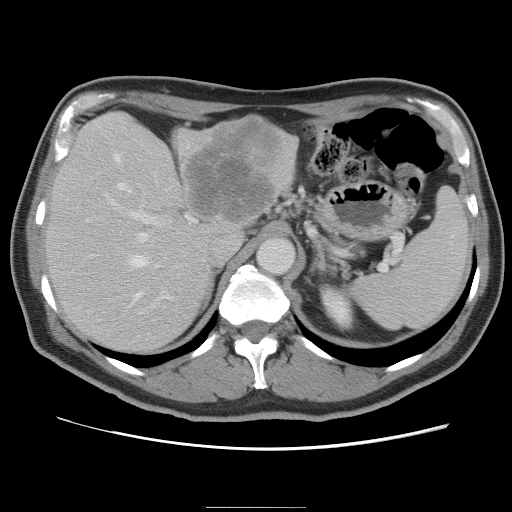
Contrast-enhanced abdominal CT, one axial slice. Slice 55 of 87 in the series (ordered by position). 120 kVp. Intravenous contrast given. Soft-tissue window (W 400 / L 40 HU). 5 mm slice thickness. 512 × 512 image matrix. Male patient, age 63 years. From the clinical record (not read from this slice): diagnosis: colorectal cancer liver metastases, imaged before liver resection; multiple liver metastases: no; largest metastasis: 9 cm.
Outlined on this slice (outlined manually by an expert reader):
- hepatic veins: box from (x=114, y=154) to (x=160, y=322) px
- liver: (x=44, y=114)–(x=298, y=354)
- planned liver remnant (the part of the liver to remain after resection): (x=44, y=149)–(x=213, y=354)
- portal vein (with intrahepatic branches): (x=96, y=193)–(x=197, y=314)
- liver metastasis: (x=186, y=120)–(x=279, y=225)